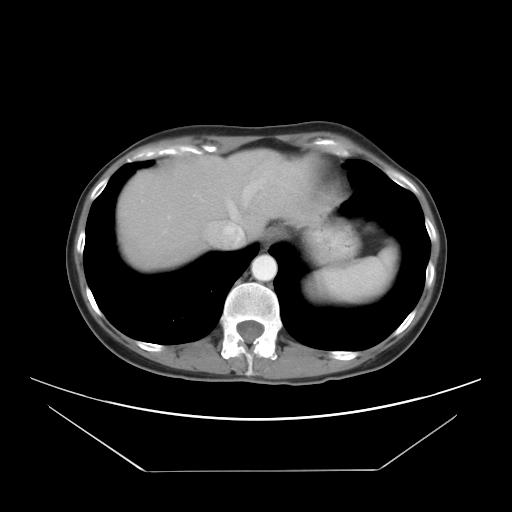
Contrast-enhanced abdominal CT, one axial slice. Position 25 of 30 along the scan axis. Reconstruction kernel STANDARD. 120 kVp. Soft-tissue window (W 400 / L 40 HU). 7.5 mm slice thickness. 512 × 512 image matrix, field of view 412 × 412 mm. Female patient, age 54 years. Case-level facts recorded for this patient, not image findings: diagnosis: colorectal cancer liver metastases, imaged before liver resection; multiple liver metastases: yes; largest metastasis: 2.5 cm; disease in both lobes: yes.
Annotated regions visible in this slice (outlined manually by an expert reader):
- hepatic veins: bounding box (x1, y1, x2, y2) in pixels: (210, 180, 261, 246)
- liver: (118, 150, 307, 268)
- planned liver remnant (the part of the liver to remain after resection): (118, 154, 273, 268)